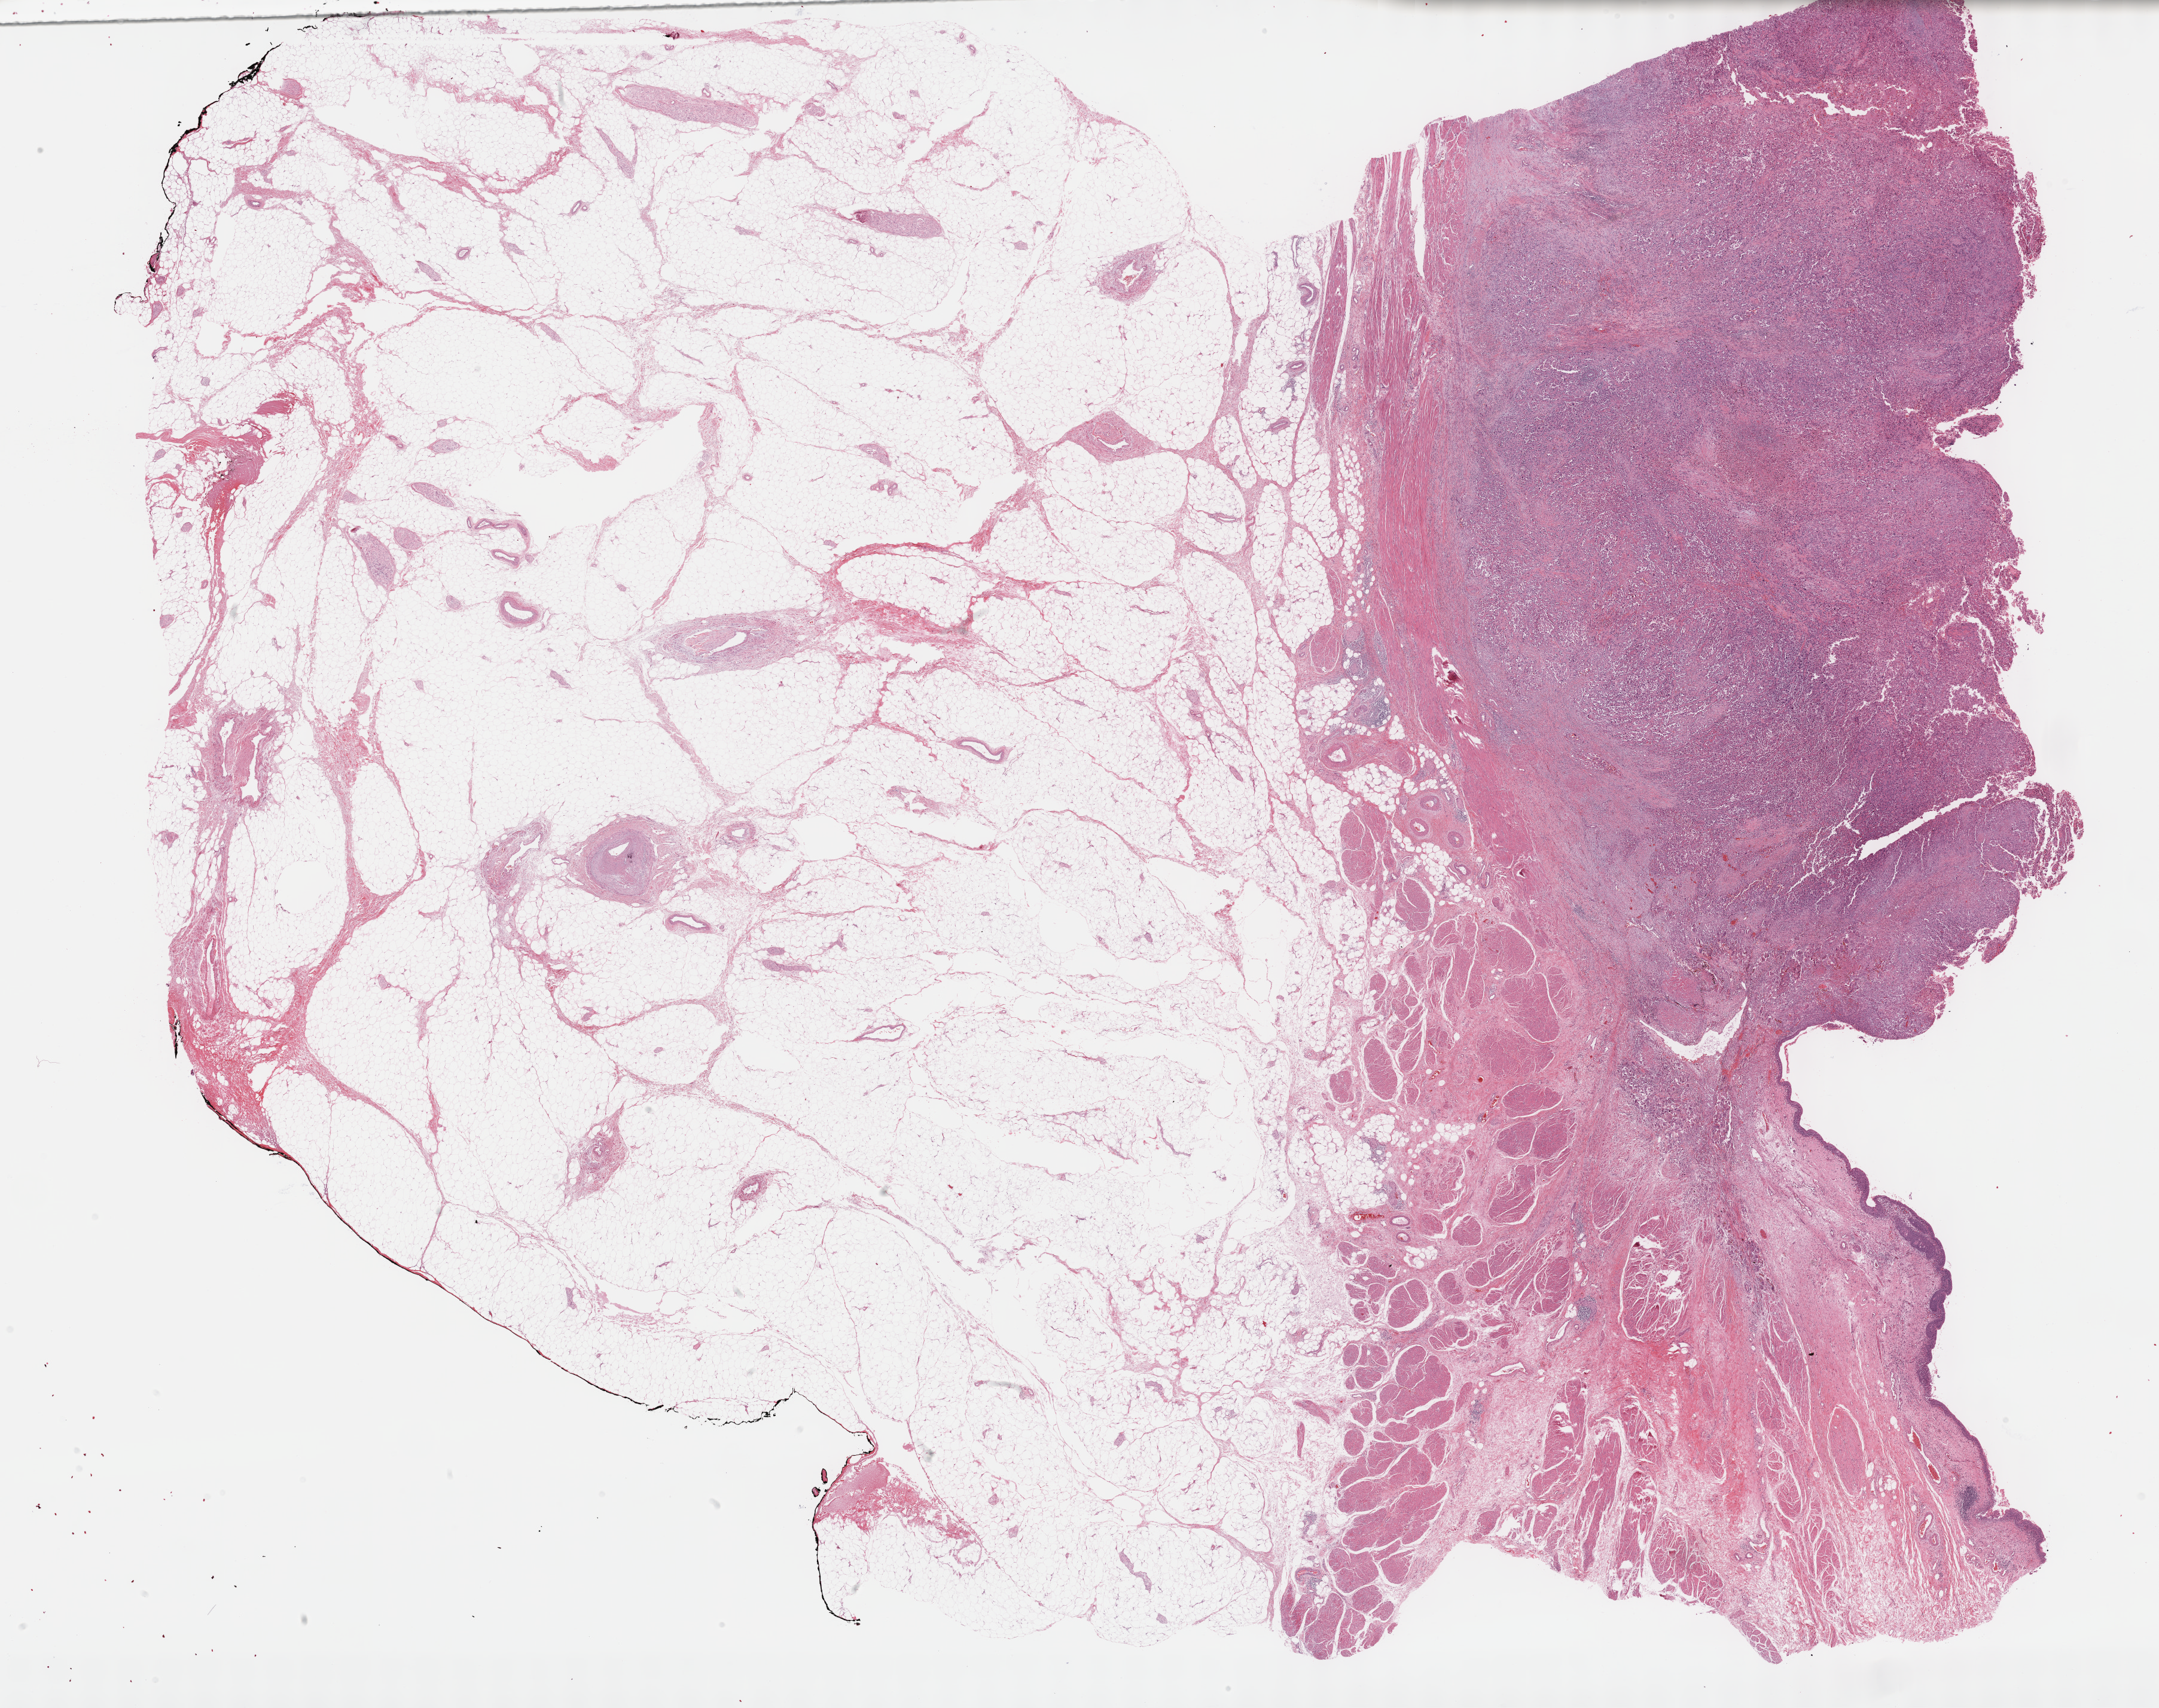
Hematoxylin and eosin (H&E) stained whole-slide image, shown as a low-resolution overview of the whole scanned area (about 29.2 x 23.1 mm, acquisition: 40x scan); formalin-fixed paraffin-embedded (FFPE) diagnostic section; sample: primary tumour, bladder. Female, age 79 years at initial diagnosis.
Diagnosis: Transitional cell carcinoma.